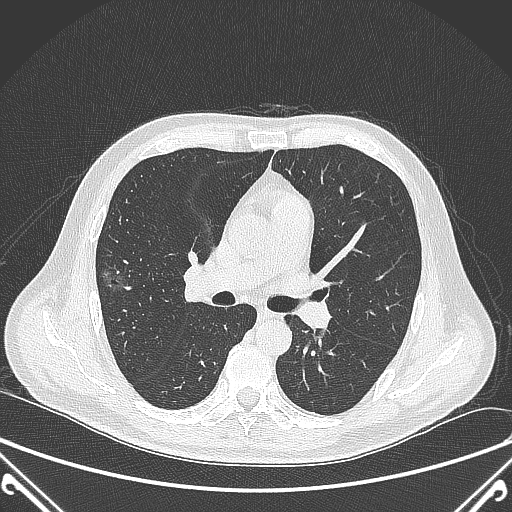
Chest CT, one axial slice; position 219 of 360 along the scan axis; 120 kVp; lung window (W 1500 / L -600 HU); 512 × 512 image matrix. Male patient, age 64 years. Case-level facts recorded for this patient, not image findings: clinical TNM (as recorded): T1c N0 M0; histopathological grade: G2.
Outlined on this slice (rectangle marked by the reading radiologist):
- lung tumour (recorded histology: adenocarcinoma): bounding box <104,261,131,291> (left, top, right, bottom; pixels)